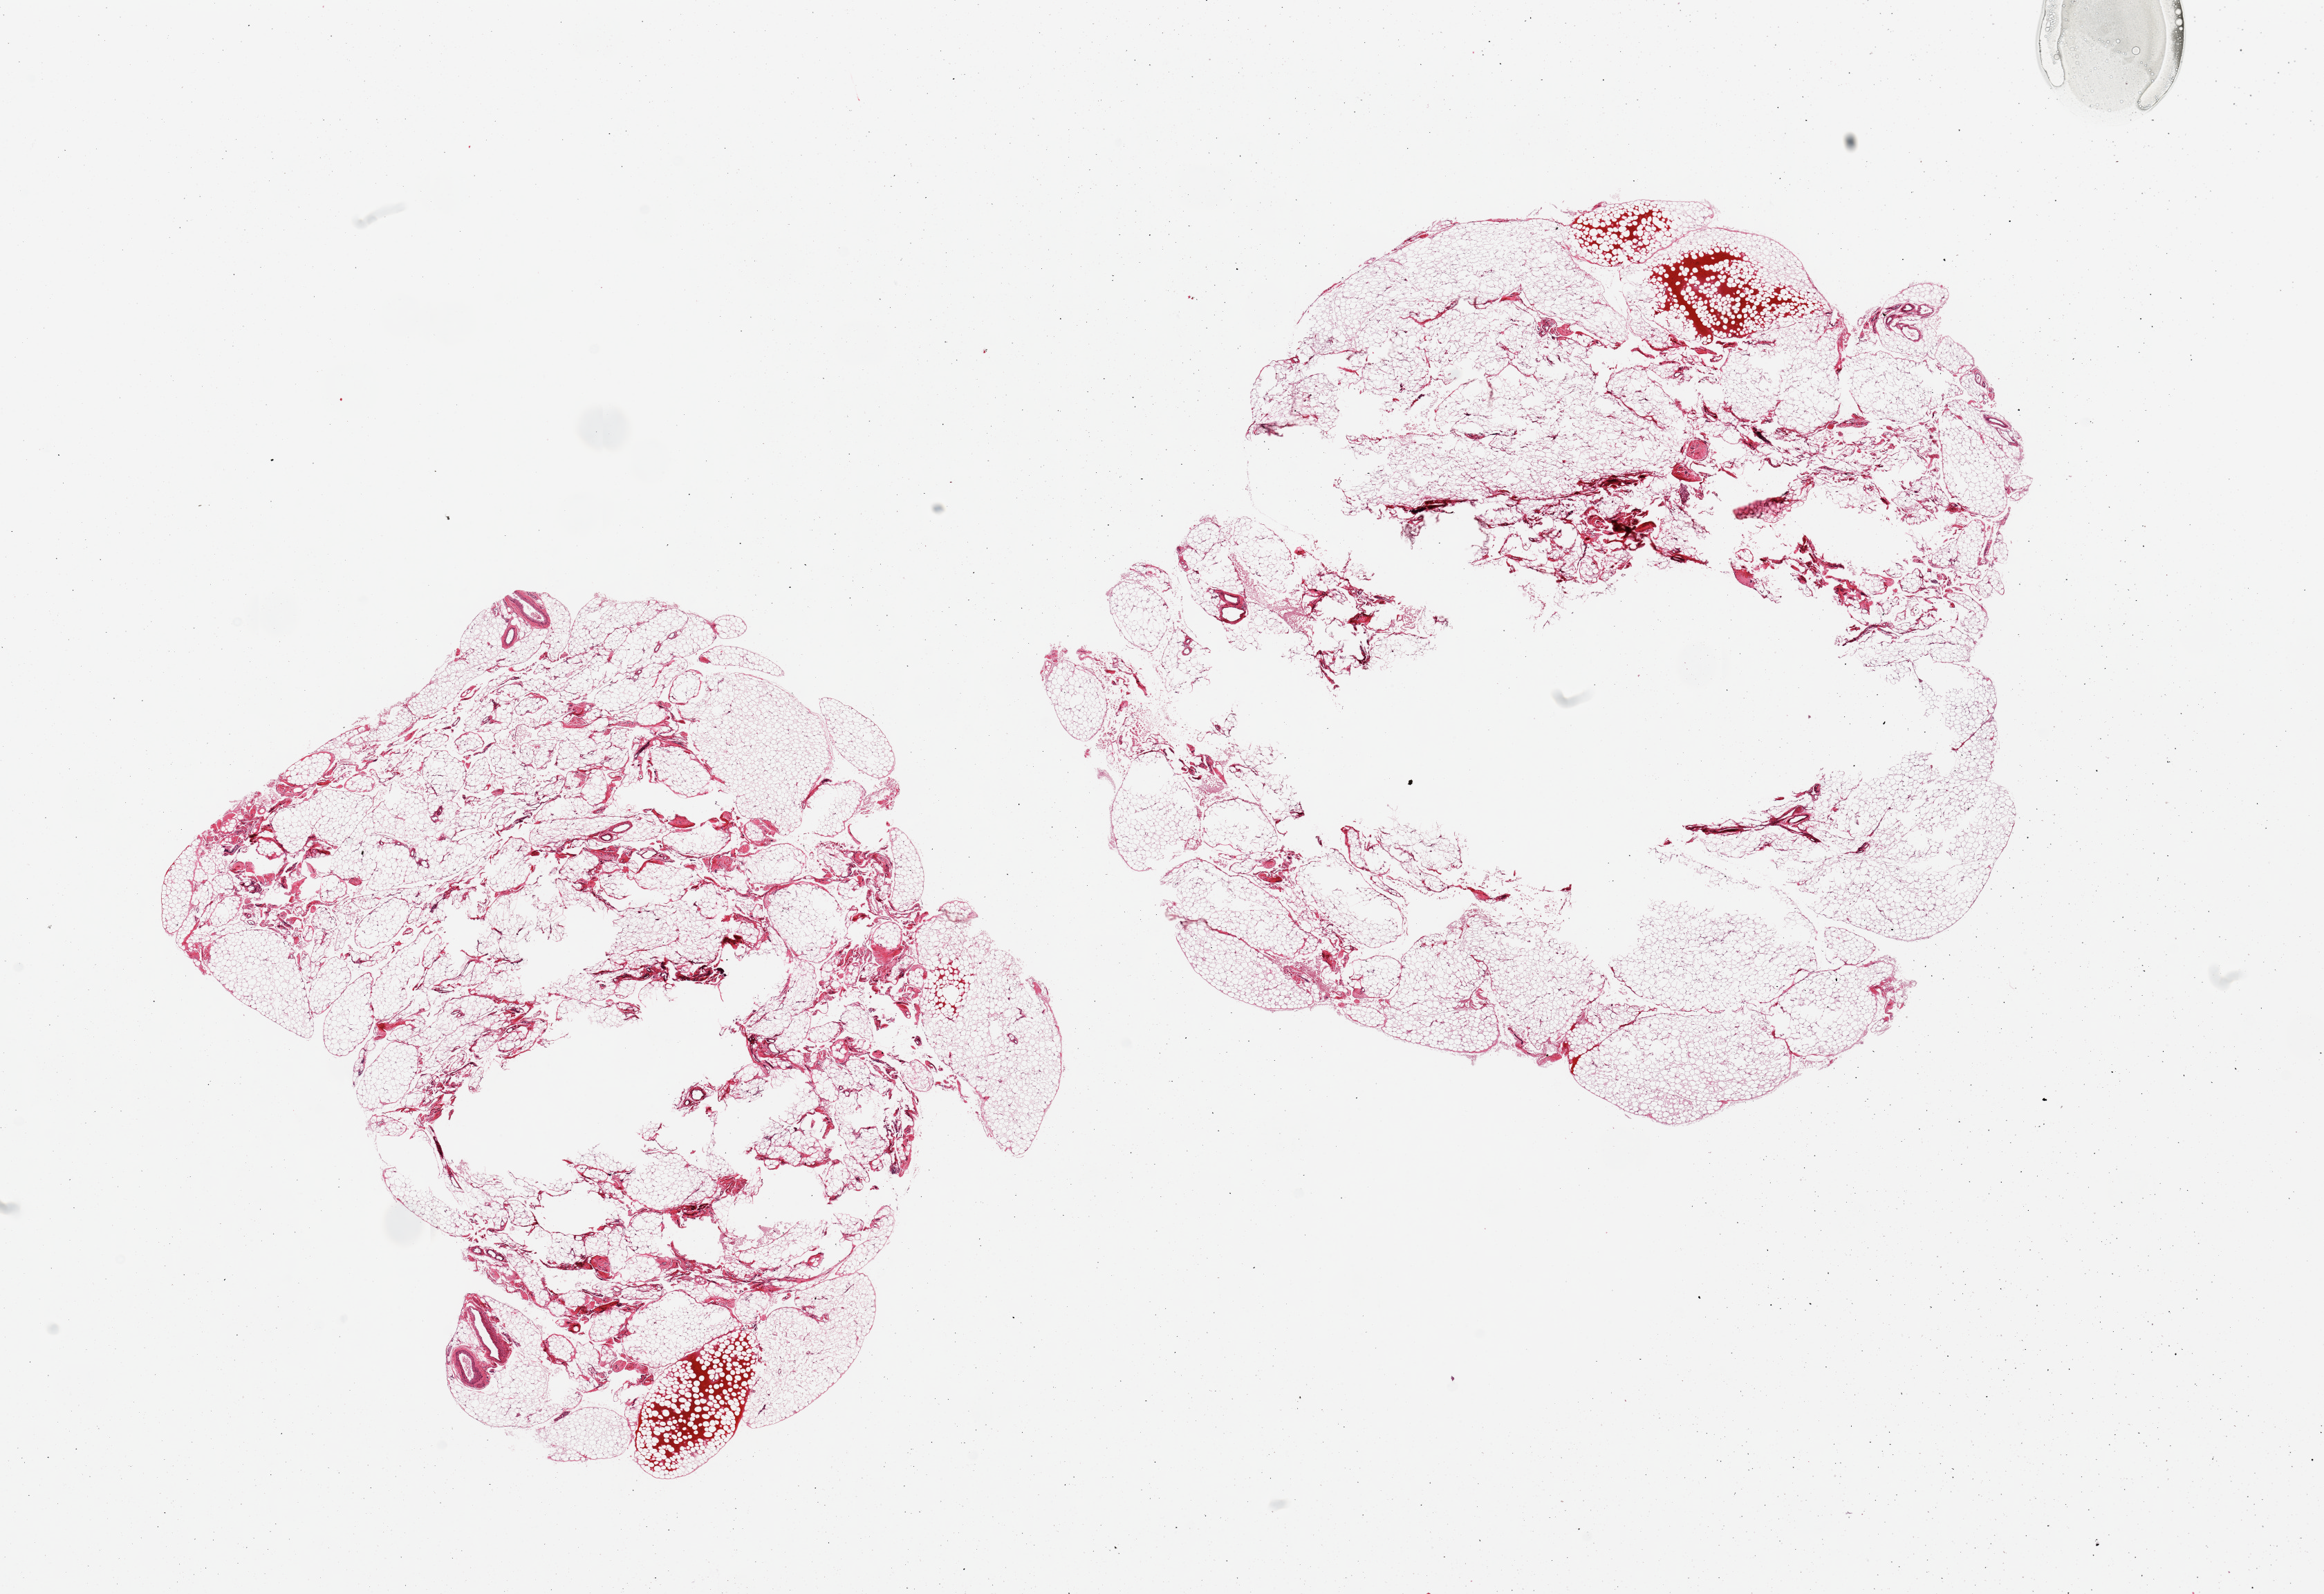
Hematoxylin and eosin (H&E) whole-slide image, brightfield — a low-resolution overview of the entire scanned area, about 26.6 x 18.2 mm. PAXgene-fixed, paraffin-embedded tissue. Section of omentum (target tissue). Donor tissue sample.
- review note (as recorded): 2 pieces, ~10% interstitial mesothelial hyperplasia